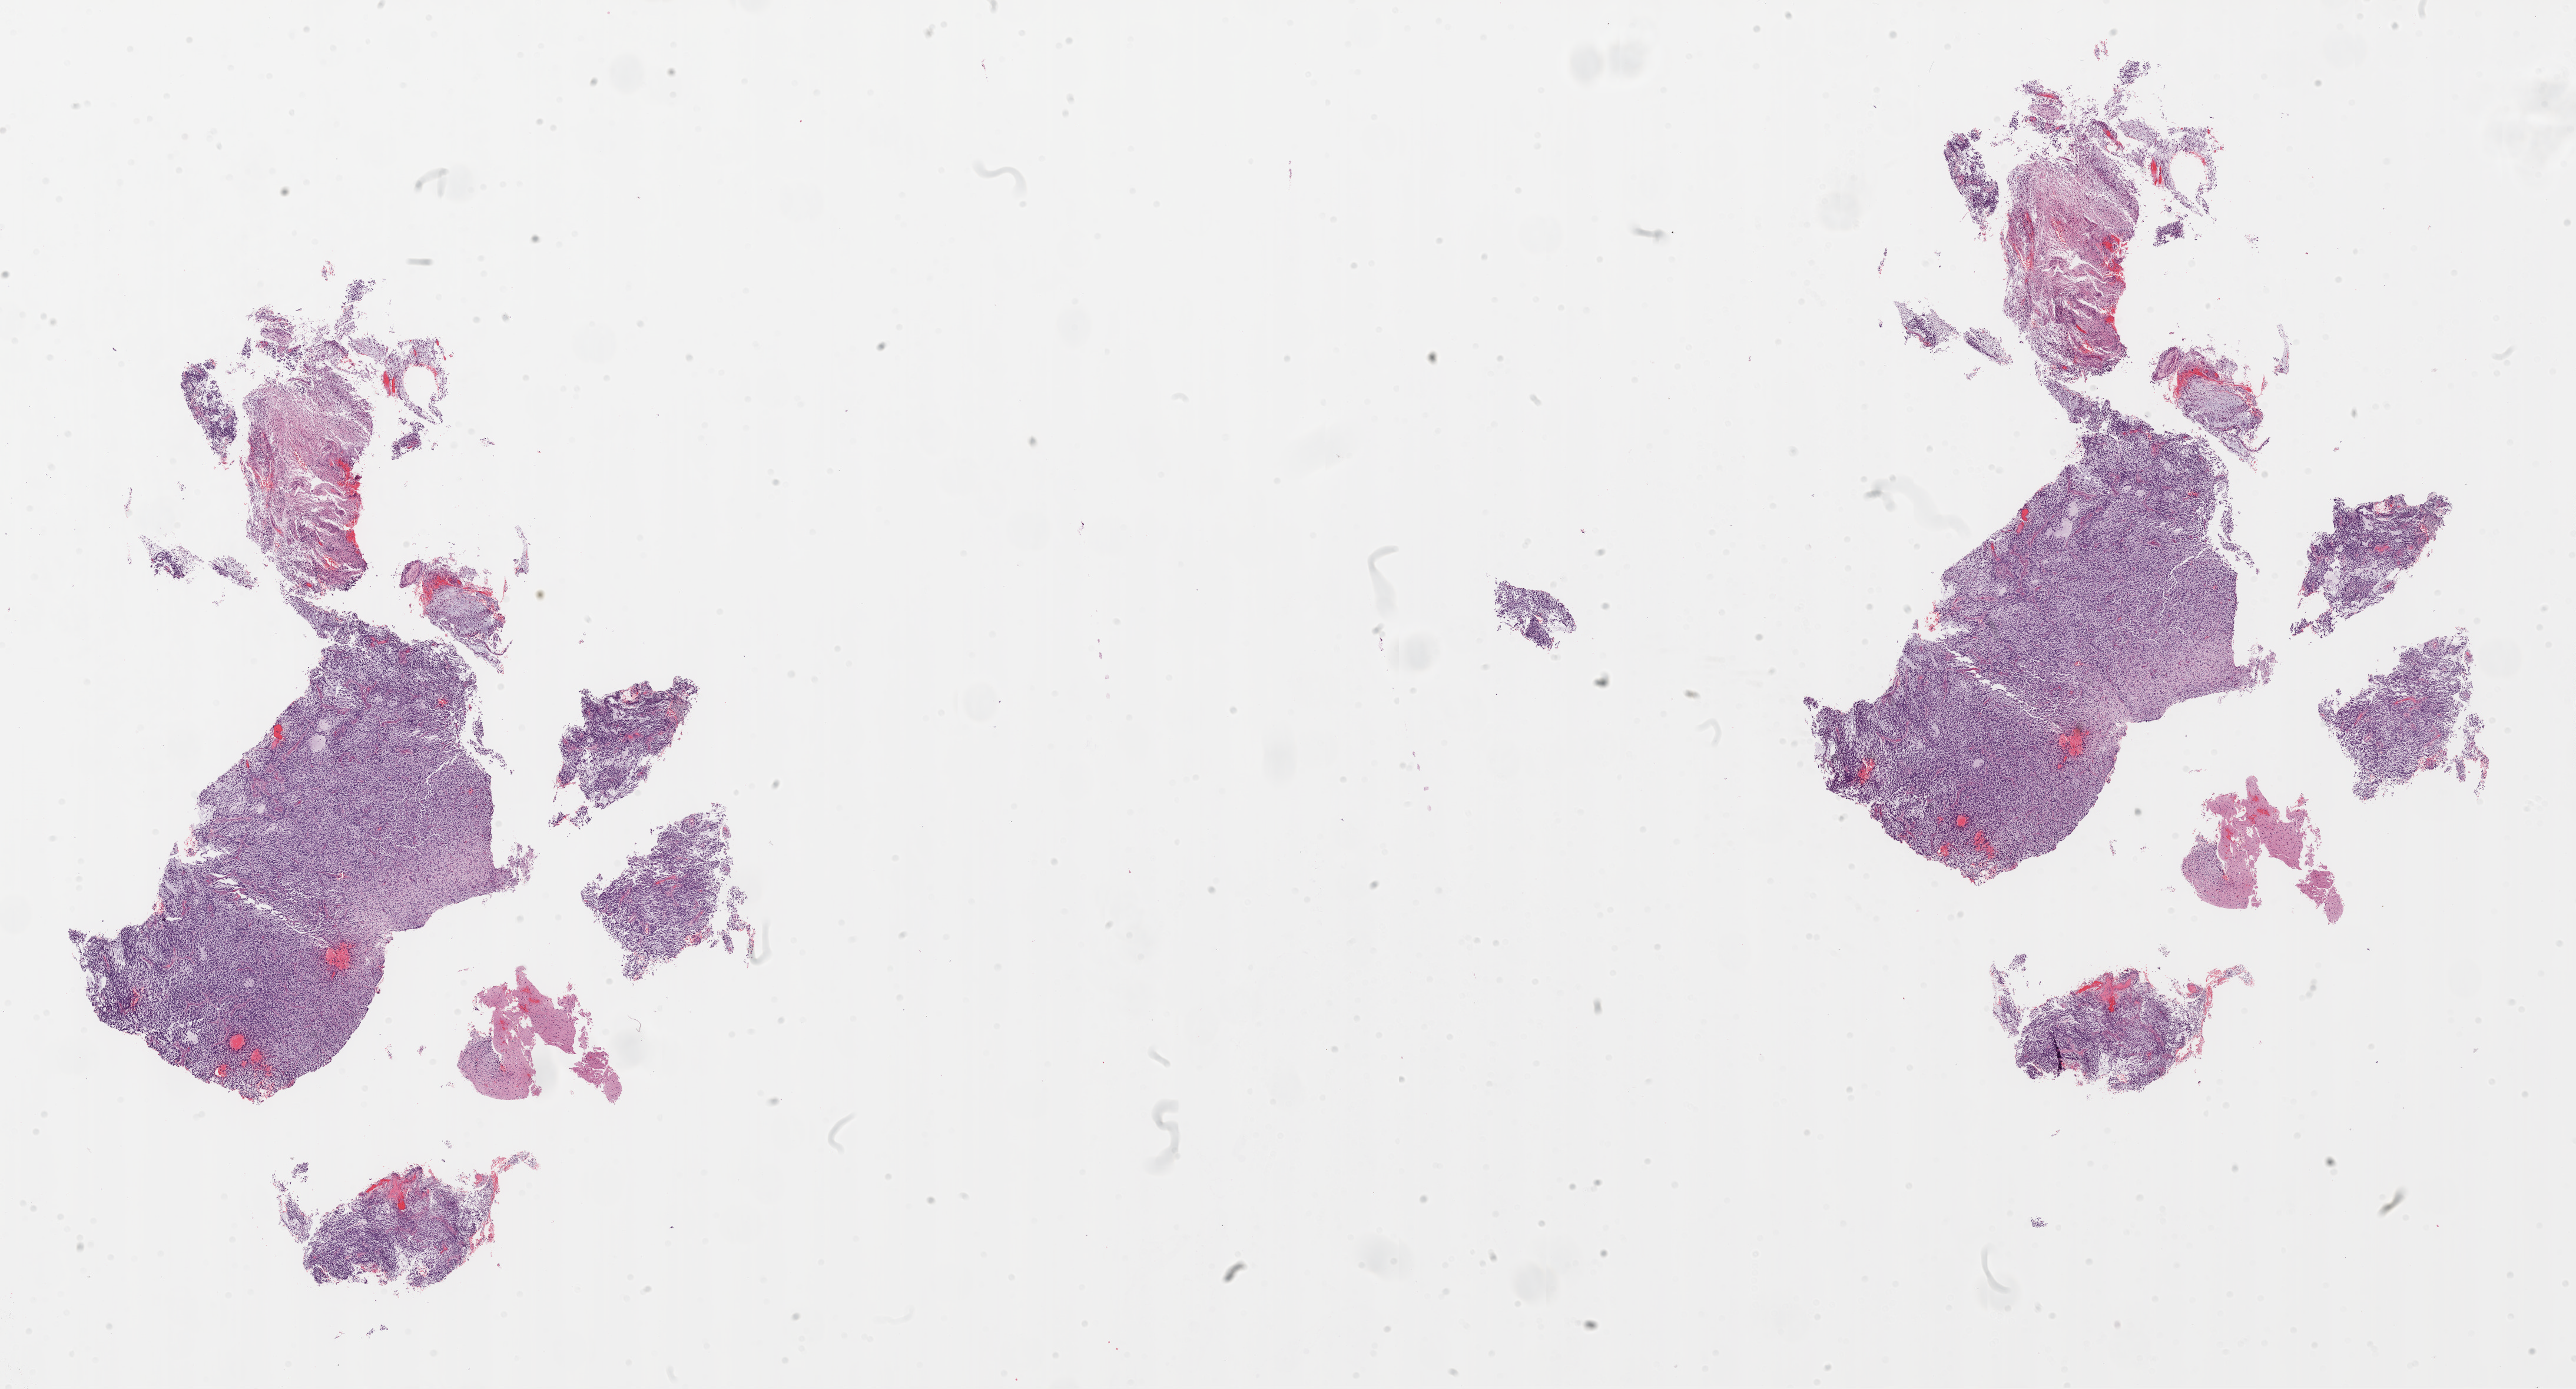
Hematoxylin and eosin (H&E) stained whole-slide image — whole scanned area (about 35.1 x 18.9 mm, acquisition: 20x scan) shown as a low-resolution overview, FFPE section, primary tumour sample from the brain. Female, age 17 years at initial diagnosis.
- diagnosis: Glioblastoma